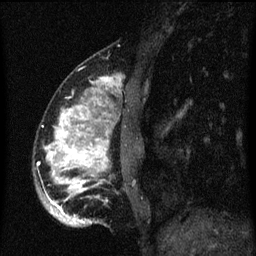
Breast MRI (dynamic contrast-enhanced), one sagittal slice. Slice 18 of 60 in the series (ordered by position). Dynamic contrast-enhanced series, image 2 of 3 at this slice position (ordered by acquisition). 1.5 T. TE 4.2 ms, TR 8.4 ms. 2 mm slice thickness. 256 × 256 image matrix. Patient: female, 34 years. Case-level facts recorded for this patient, not image findings: setting: breast cancer imaged before/during neoadjuvant chemotherapy; receptor status: HR-positive, HER2-negative.
Outlined on this slice (semi-automatically segmented with operator editing):
- analysis volume of interest (the breast-tissue region the enhancement analysis was run in; not a lesion): box from (x=34, y=64) to (x=143, y=227) px
- tumour enhancement mask (voxels above the 70 % enhancement threshold inside the analysis volume of interest): (x=46, y=78)–(x=117, y=225)